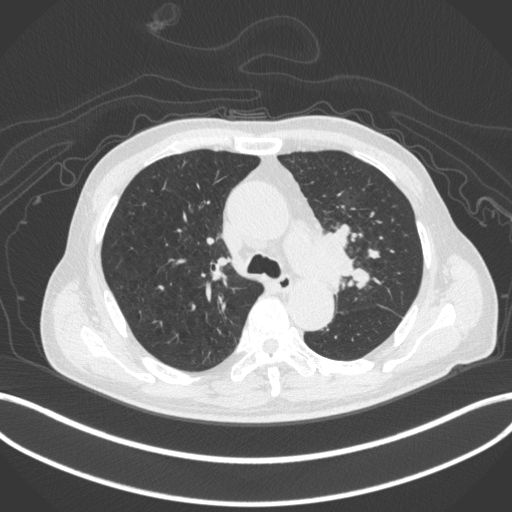
Chest CT, one axial slice. Slice 292 of 420 in the series (ordered by position). Lung window (W 1500 / L -600 HU). 512 × 512 image matrix, field of view 400 × 400 mm. Patient: male, 77 years. Case-level facts recorded for this patient, not image findings: clinical TNM (as recorded): T3 N1 M0.
Structures marked on this image (bounding box drawn by a radiologist):
- lung tumour (recorded histology: adenocarcinoma): bounding box (x1, y1, x2, y2) in pixels: (303, 223, 361, 283)